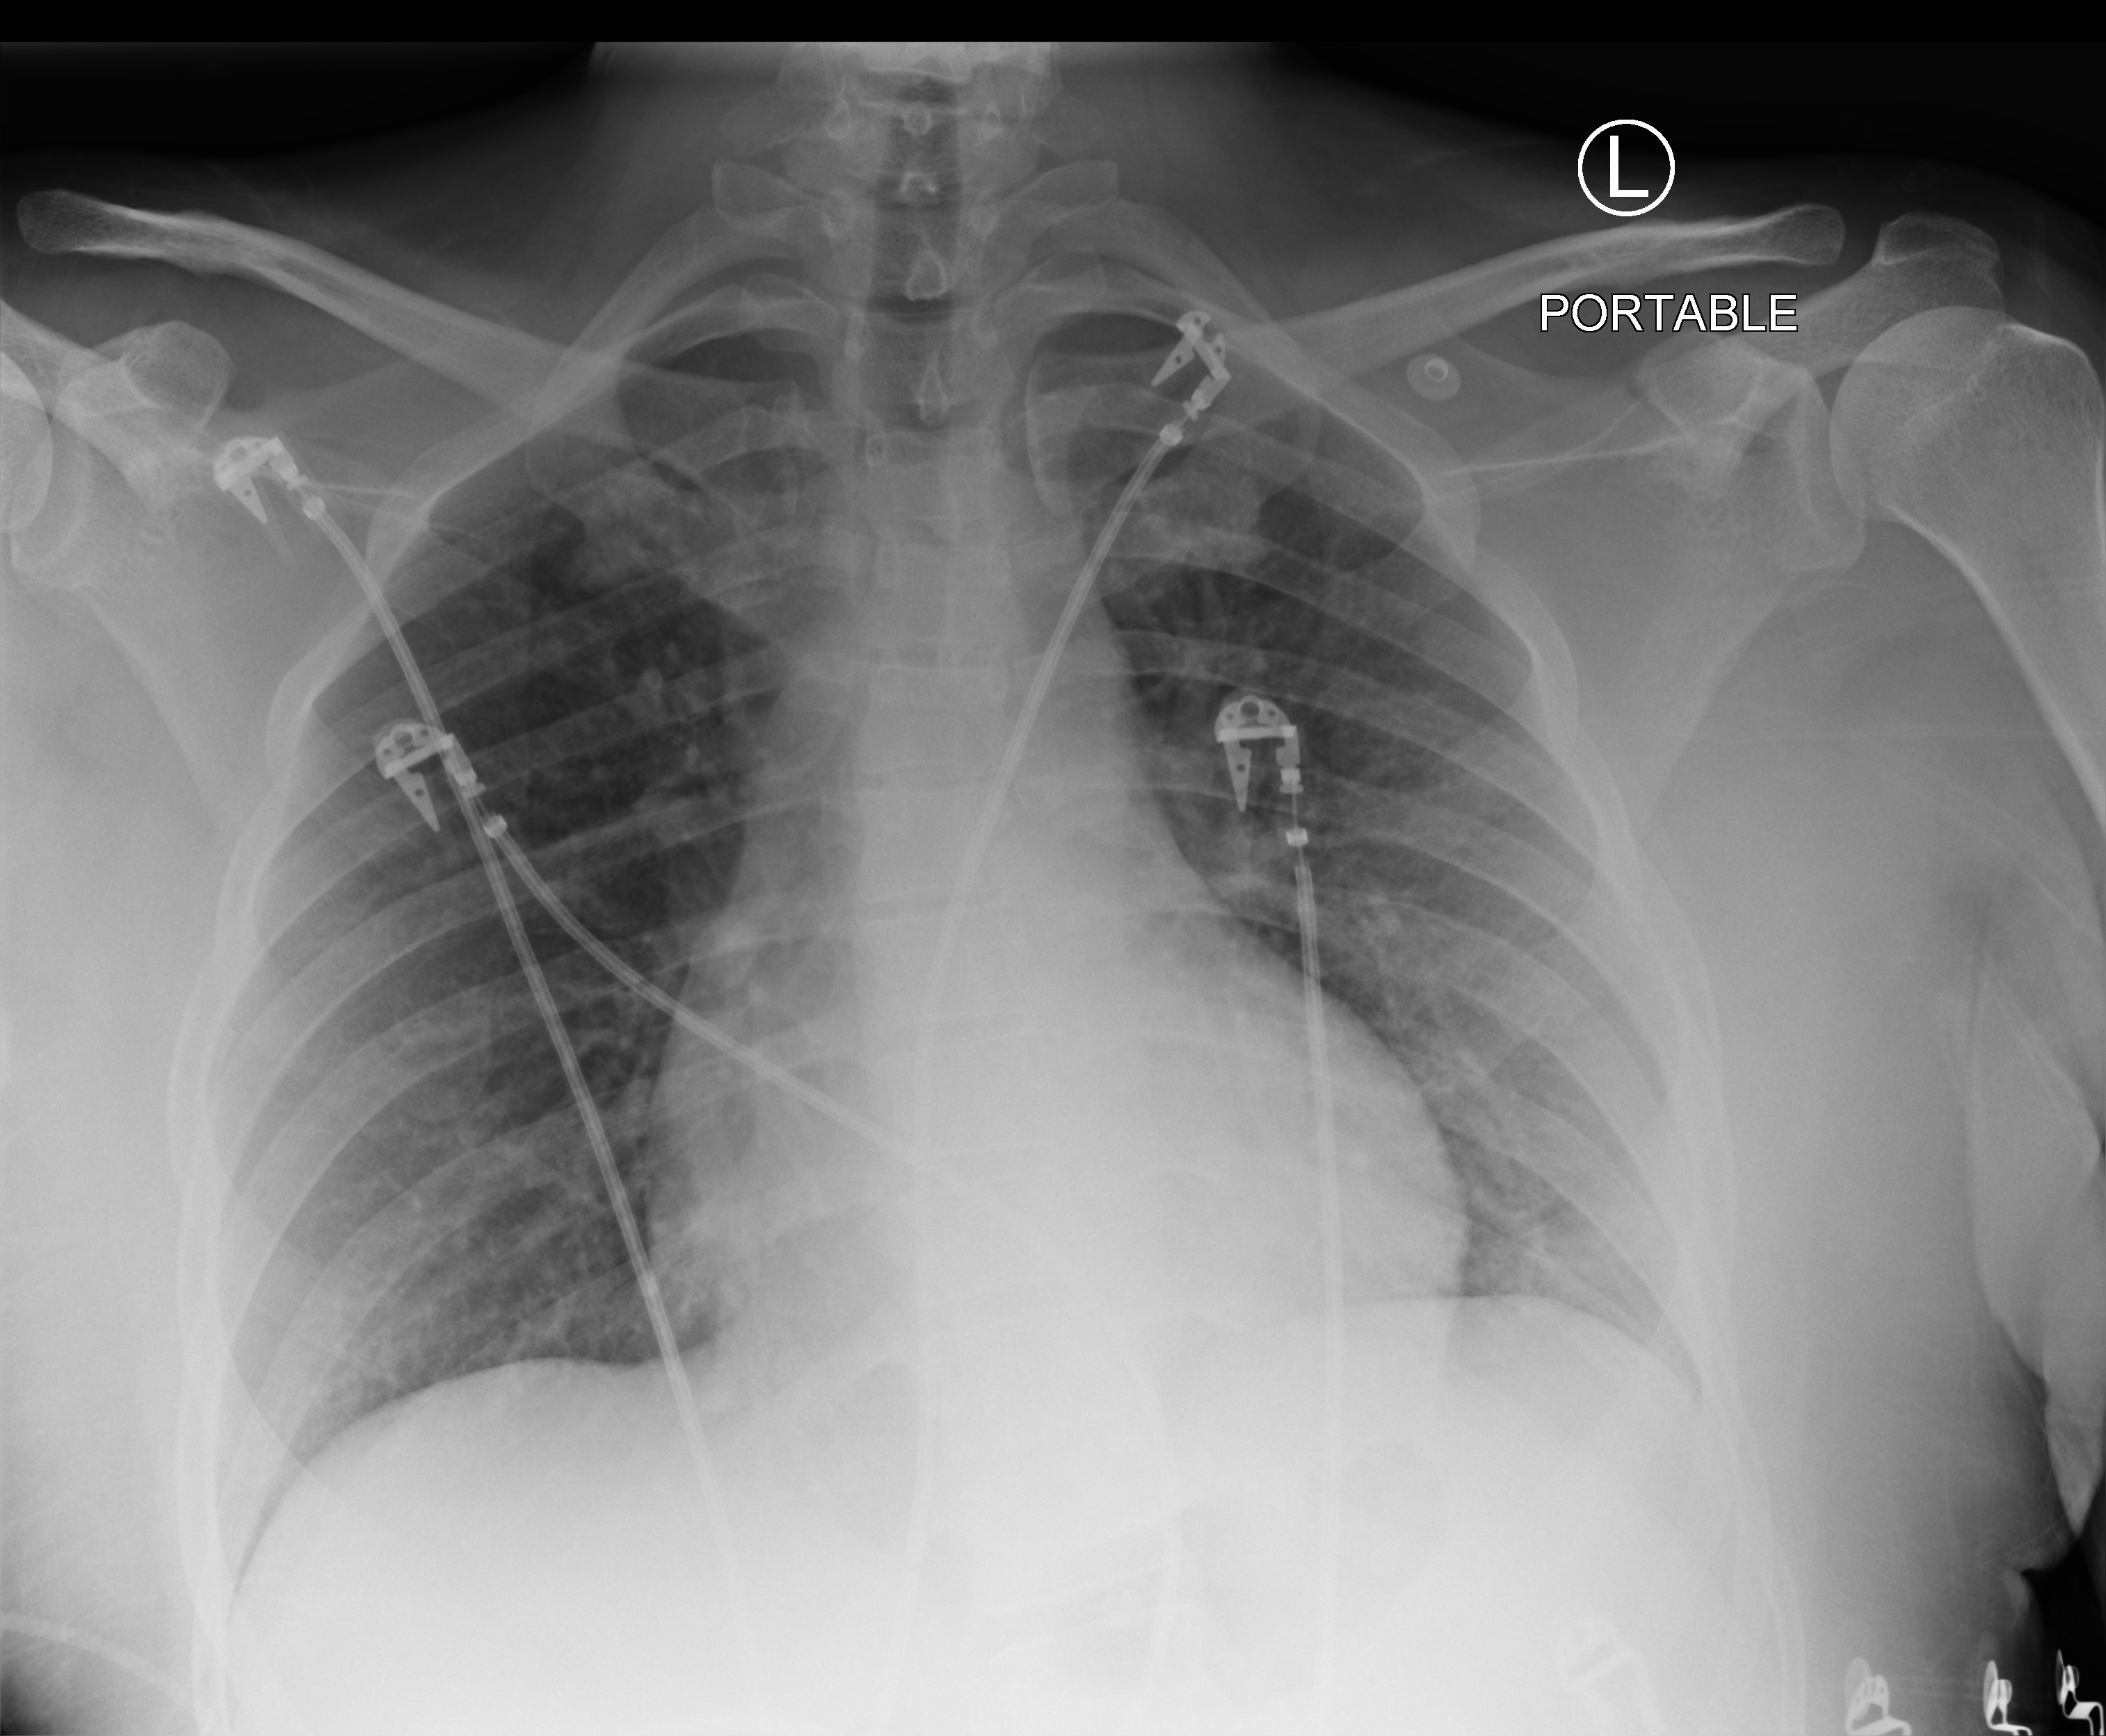
Portable chest radiograph. Patient hospitalised with COVID-19; male, aged 18–59 years.
Hospital-stay facts (about this admission, not read from this image; timing relative to this image not recorded):
- COPD (admission record): no
- mechanically ventilated during this hospital stay: no